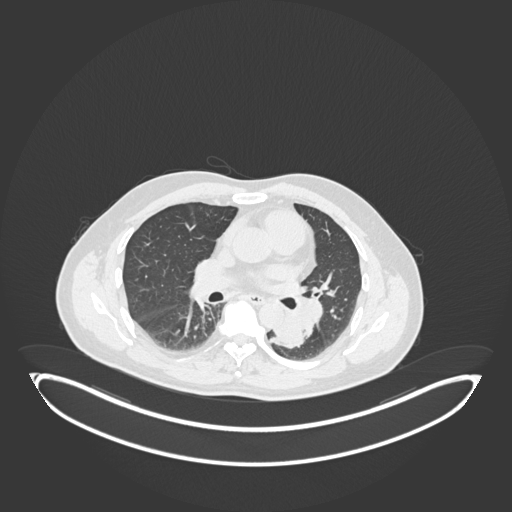
Chest CT, one axial slice. Slice 108 of 258 in the series (ordered by position). Reconstruction kernel B30f. 120 kVp. Lung window (W 1500 / L -600 HU). 1 mm slice thickness. 512 × 512 image matrix, field of view 500 × 500 mm. Male patient, age 54 years. Case-level facts recorded for this patient, not image findings: clinical TNM (as recorded): T3 N0 M0.
Annotated regions visible in this slice (rectangle marked by the reading radiologist):
- lung tumour (recorded histology: squamous cell carcinoma): box from (x=269, y=308) to (x=309, y=353) px